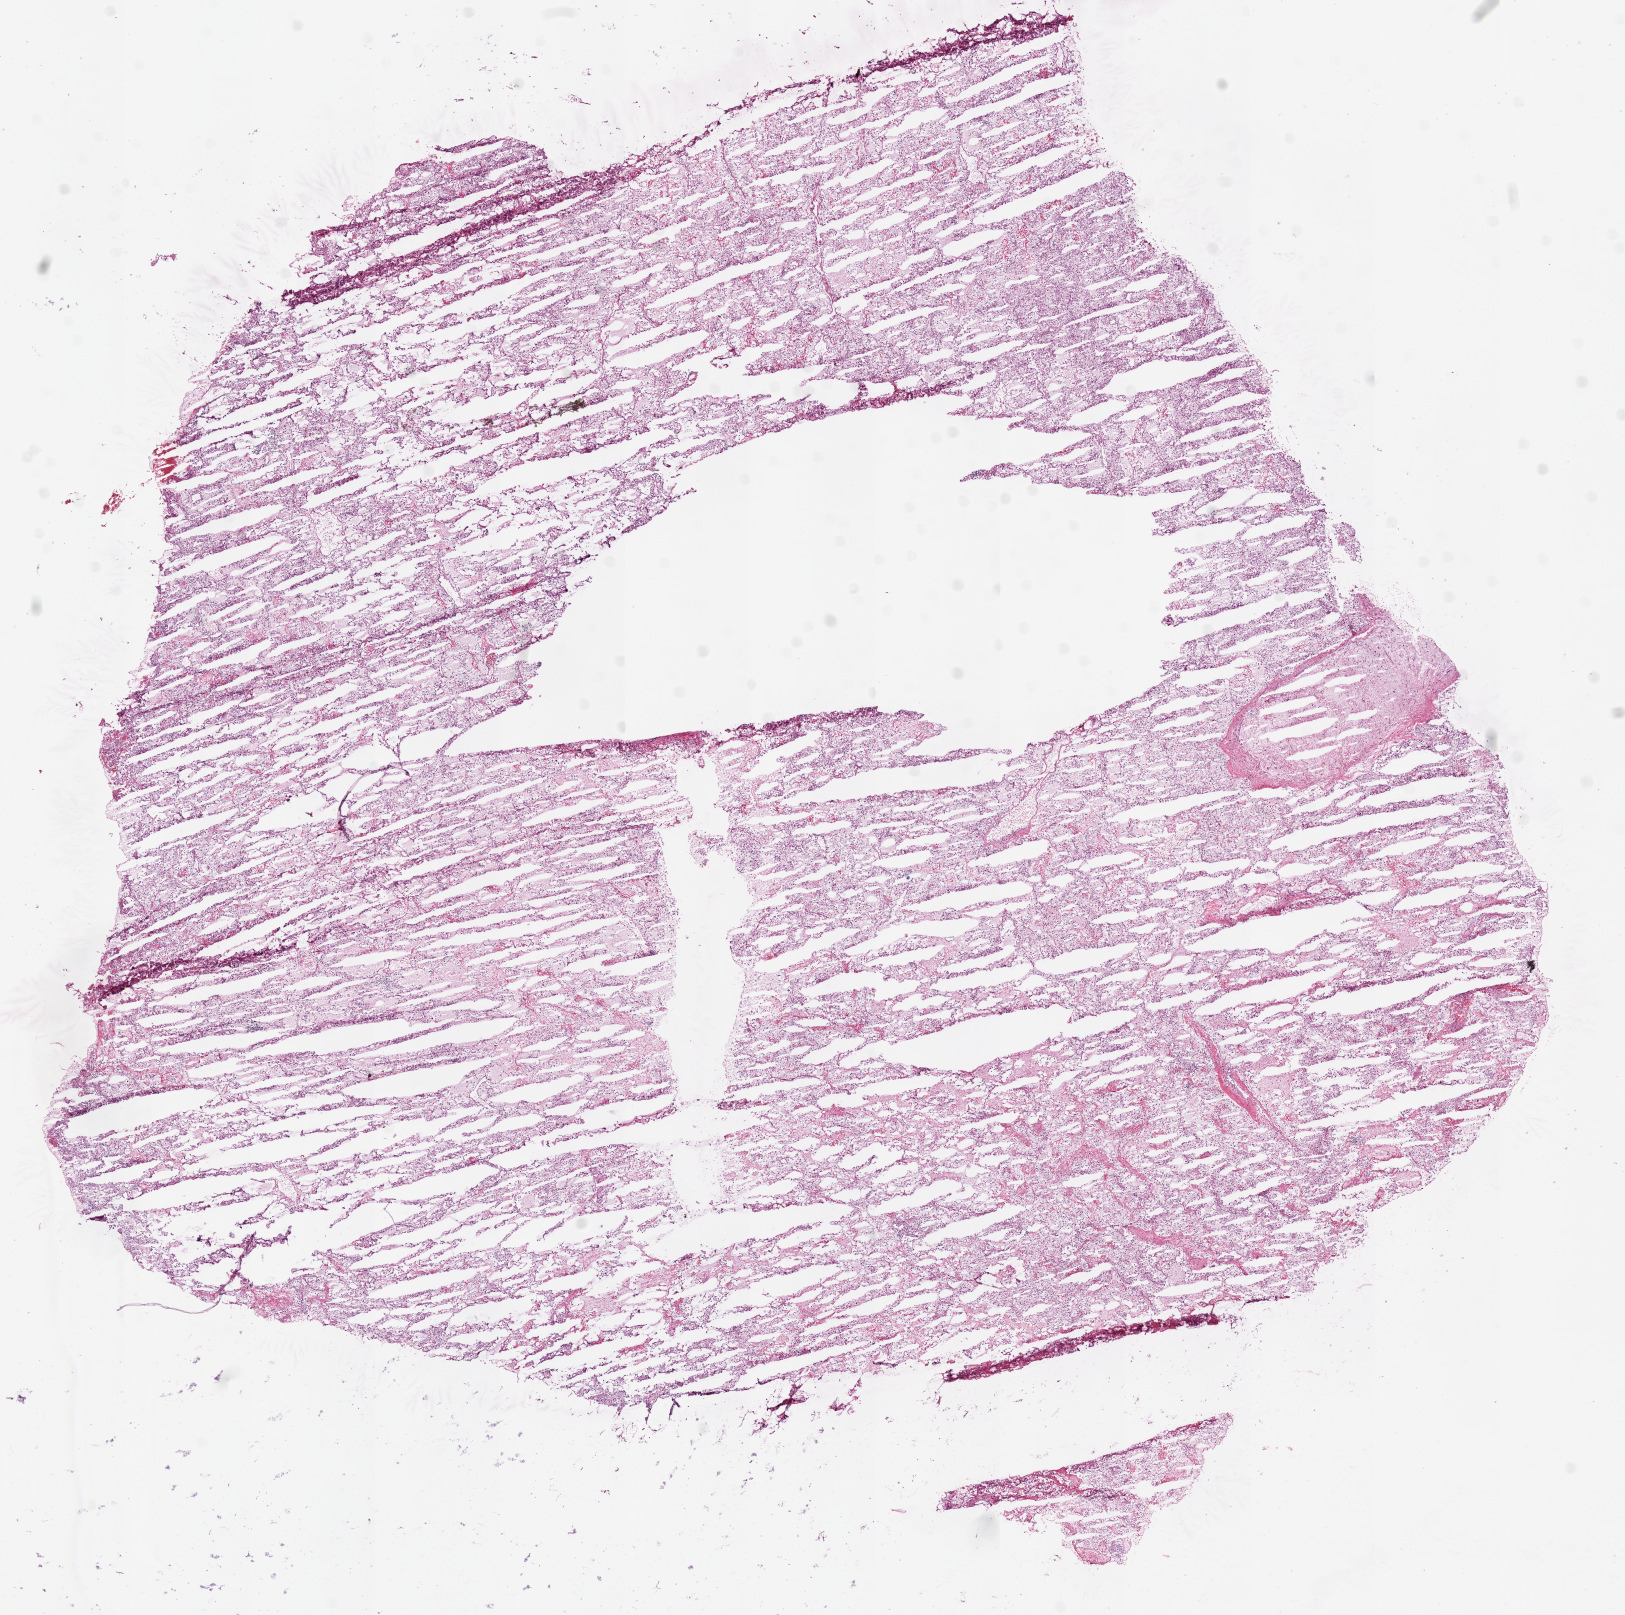
H&E whole-slide image — low-resolution overview of the scanned area, about 13.0 x 13.0 mm, frozen section, primary tumour sample from the kidney. Patient: male, age at initial diagnosis 49 years. Histologic grade: G3 (poorly differentiated). Slide review estimates, as recorded: tumour cells 95%, tumour nuclei 90%, normal cells 0%, stromal cells 5%, necrosis 0%.
- AJCC pathologic stage: II
- lymph nodes positive (case pathology): 0 of 3 examined
- diagnosis: Clear cell adenocarcinoma, NOS